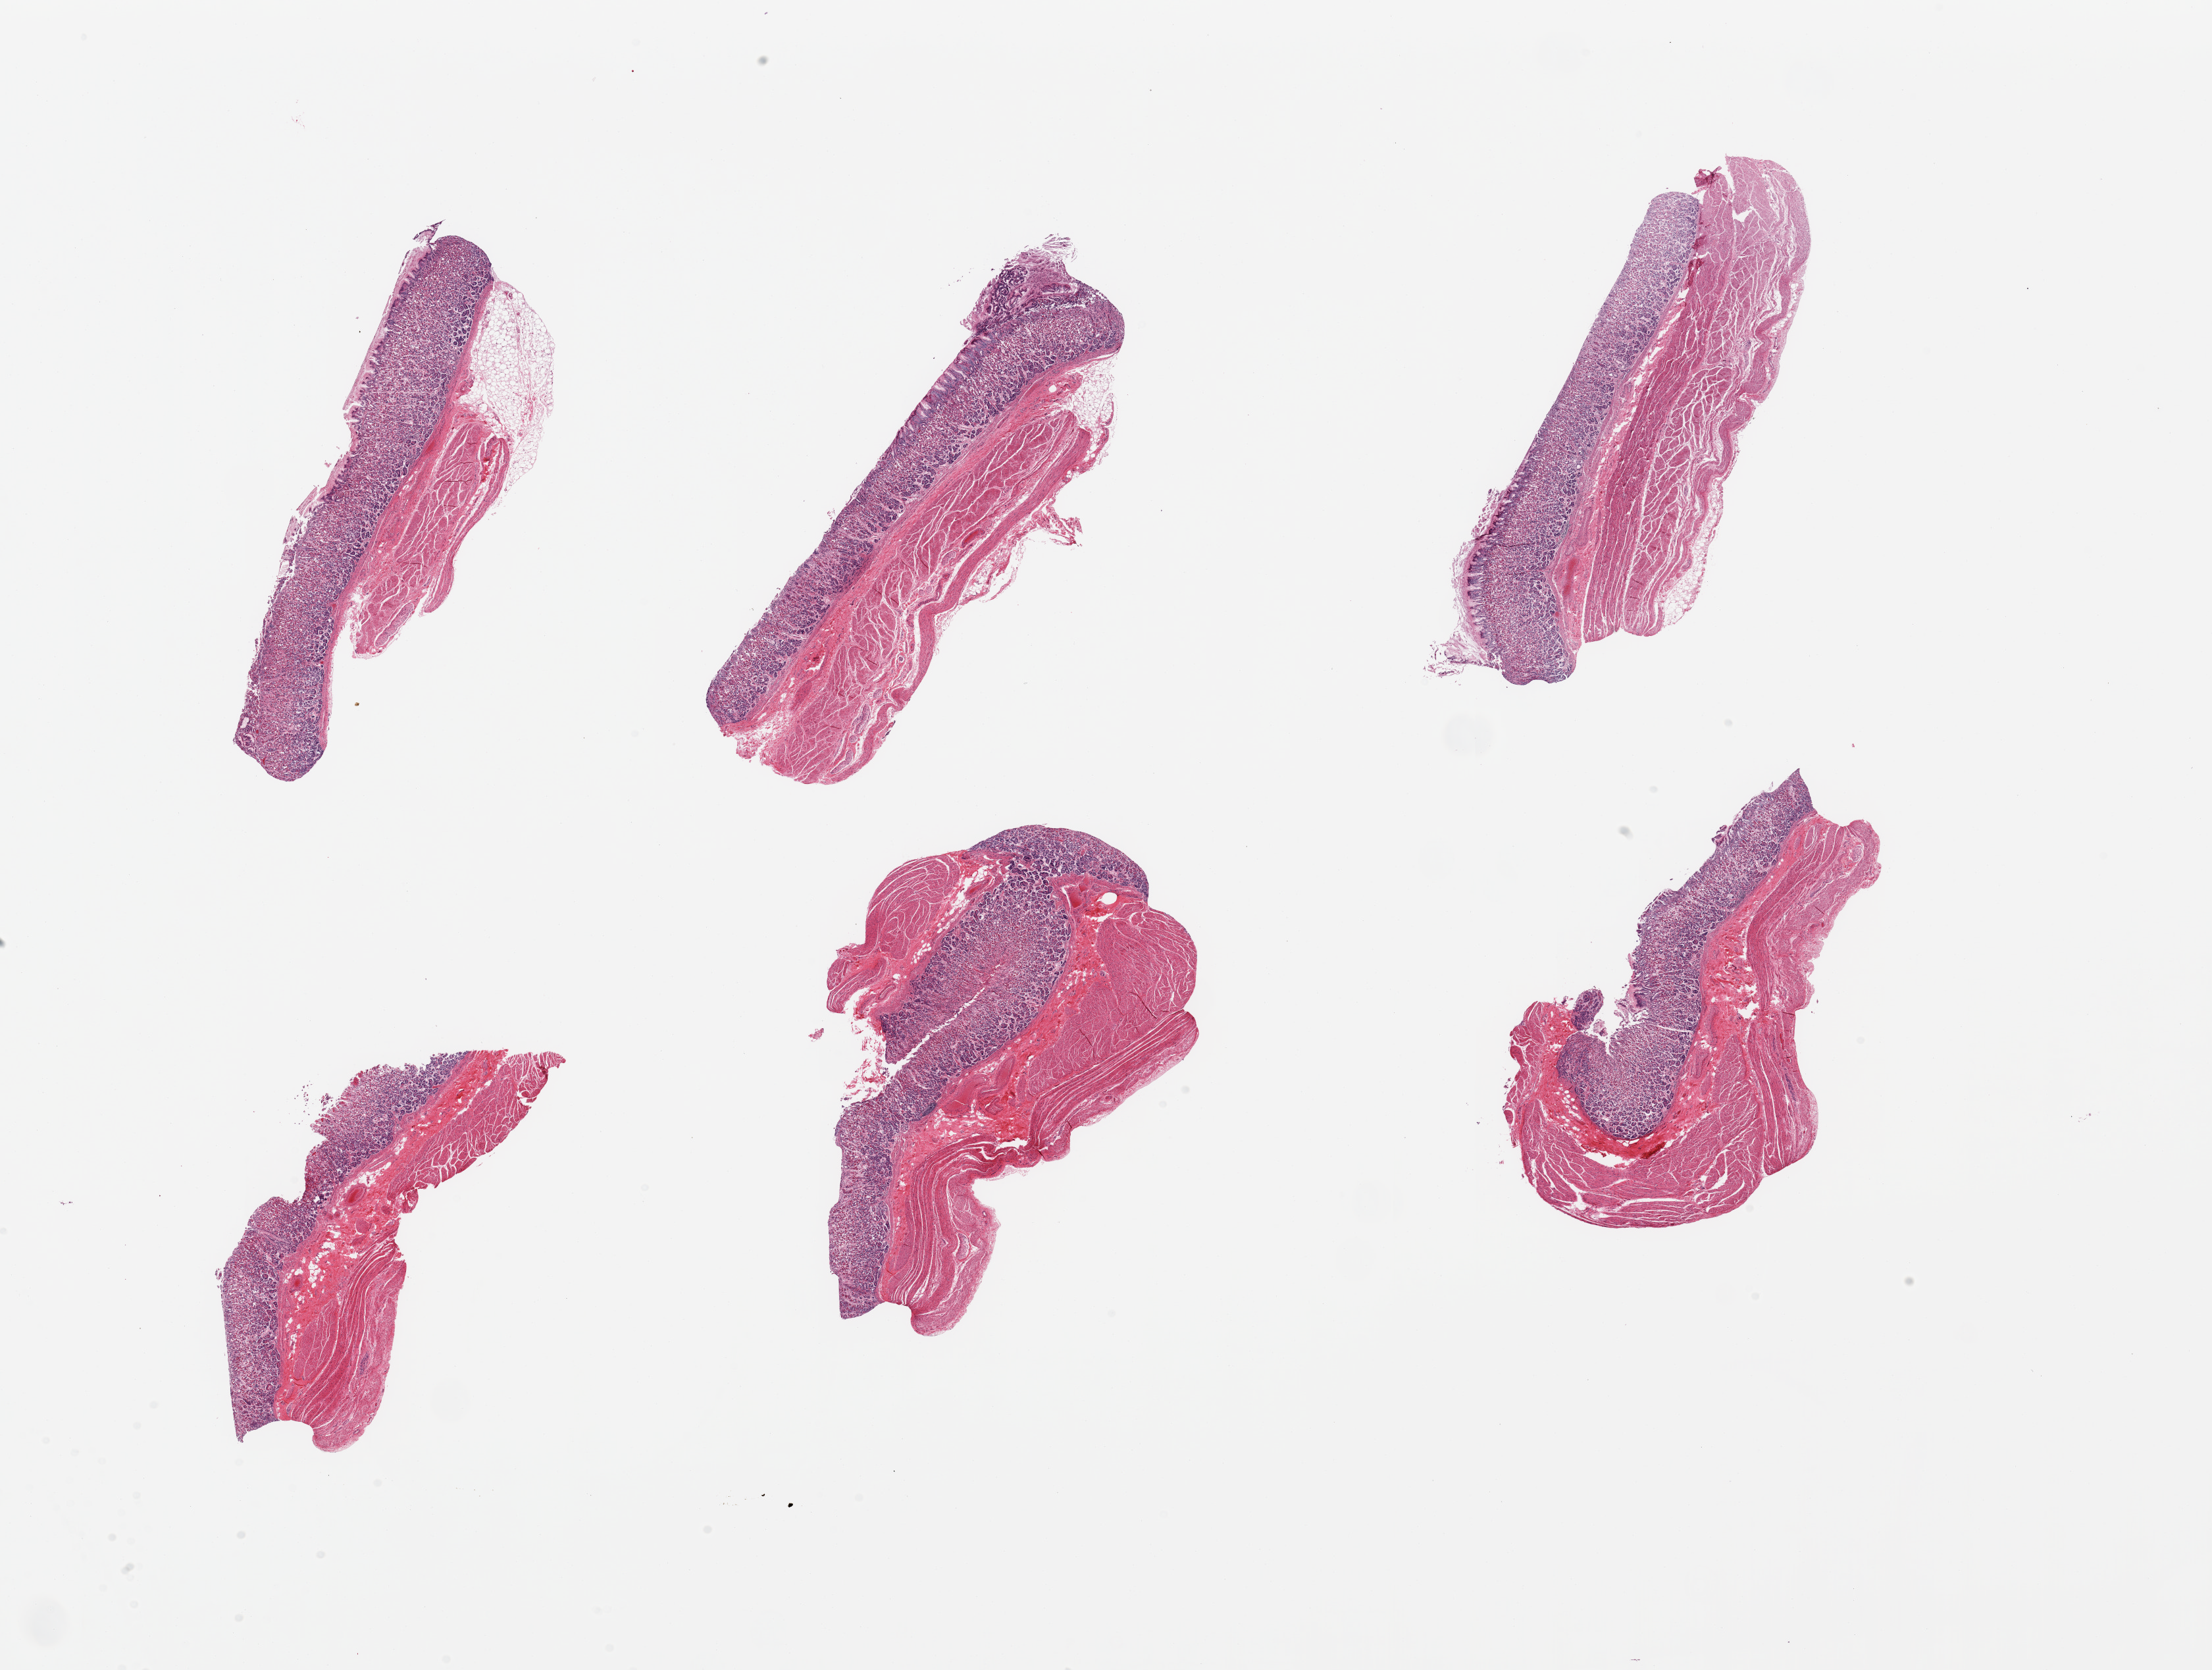
H&E whole-slide image, shown as a low-resolution overview of the whole scanned area (about 26.6 x 20.1 mm). PAXgene-fixed, paraffin-embedded tissue. Target tissue: stomach. Tissue donor sample. Female donor.
Review note (as recorded): 6 pieces; mucosa autolysis=2; muscle =1.